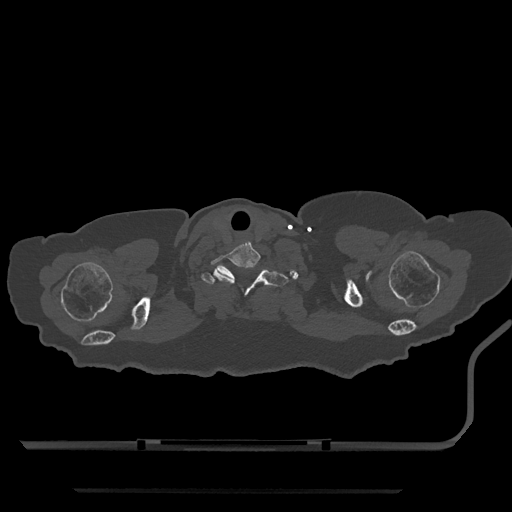
CT including the spine, one axial slice; slice 724 of 797 in the series (ordered by position); reconstruction kernel Br40s/3; 120 kVp; bone window (W 1800 / L 400 HU); 0.5 mm slice thickness; 512 × 512 image matrix, field of view 440 × 440 mm. Female patient, age 51 years. From the clinical record (not read from this slice): primary cancer: neuro; vertebrae with lytic lesions (as recorded): T8.
Outlined on this slice (semi-automatic segmentation, software-assisted and operator-edited):
- T1 vertebra: bounding box [x1, y1, x2, y2] px = [201, 265, 289, 296]